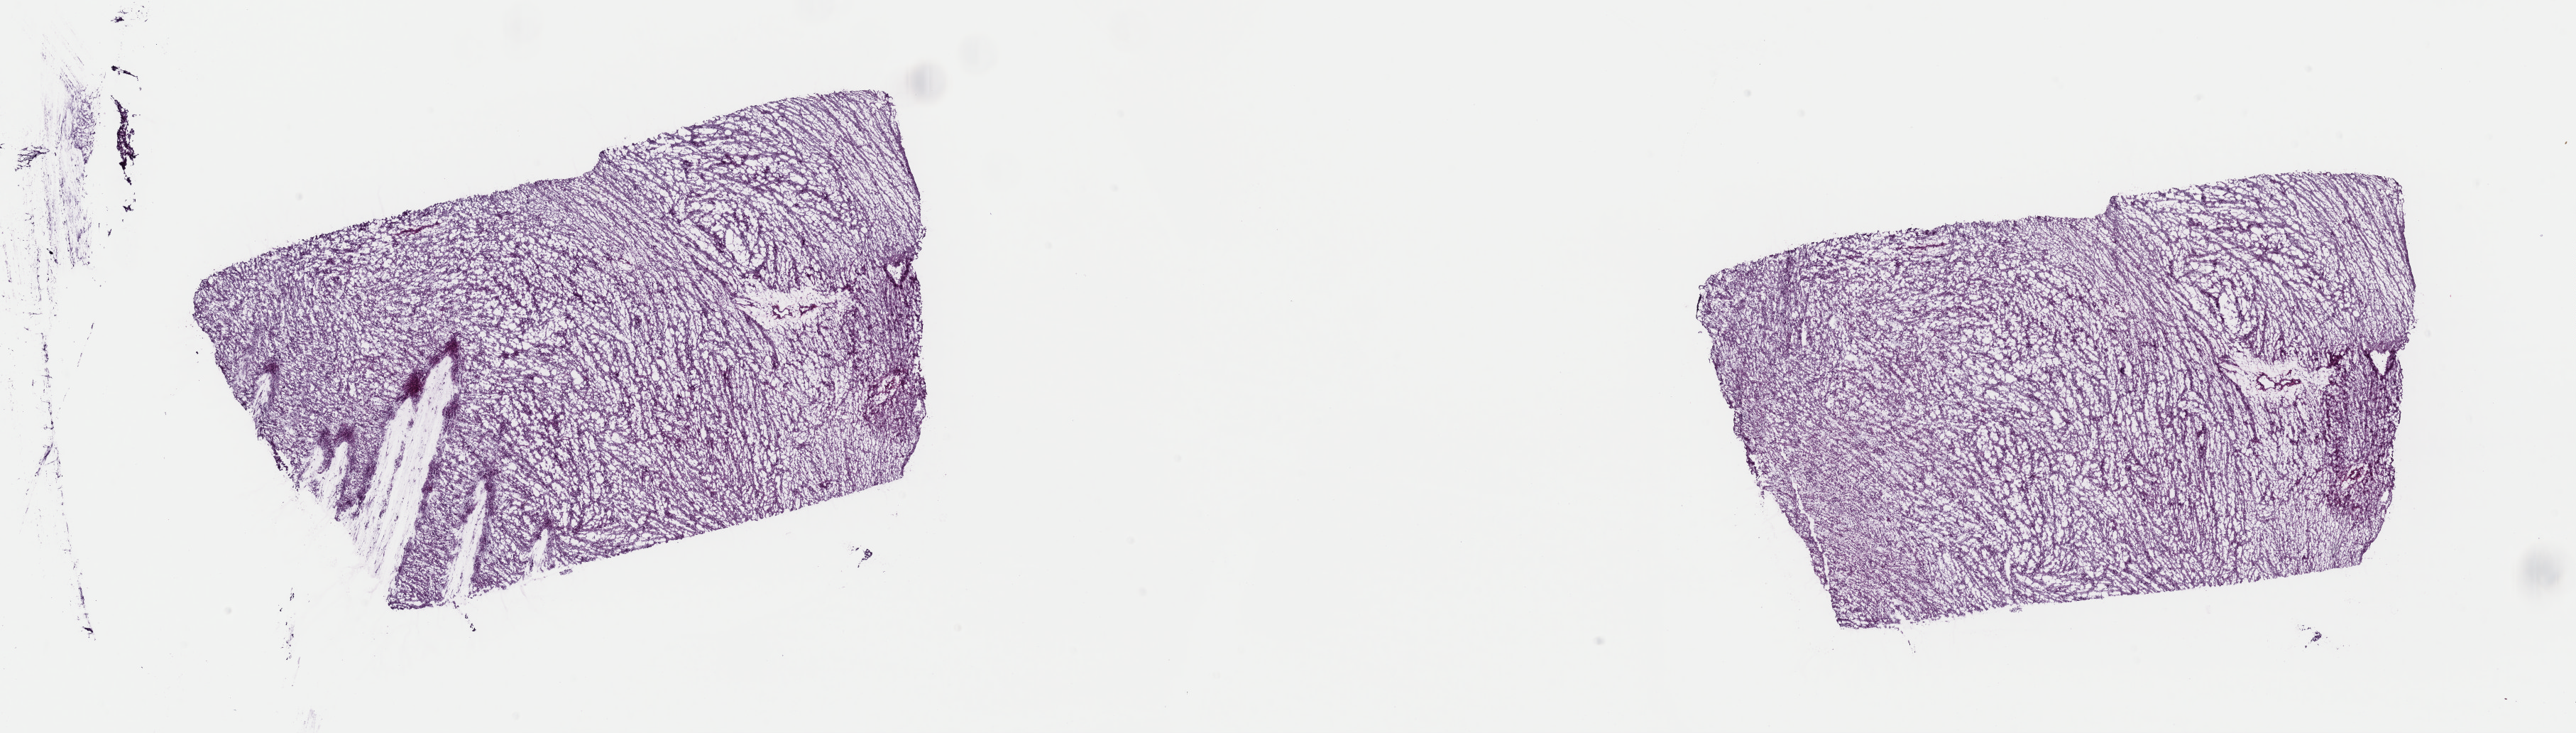
Whole-slide histology image, H&E-stained, low-resolution overview of the scanned area, about 28.7 x 8.2 mm (slide scanned at 40x); frozen section; retroperitoneum and peritoneum, primary tumour sample. Patient: male, age at initial diagnosis 52 years. Slide review estimates, as recorded: tumour cells 100%, tumour nuclei 90%, normal cells 0%, stromal cells 0%, necrosis 0%. Infiltration values recorded for this section: lymphocyte infiltration 0%, monocyte infiltration 0%, neutrophil infiltration 0%.
• histologic diagnosis: Dedifferentiated liposarcoma (retroperitoneum)